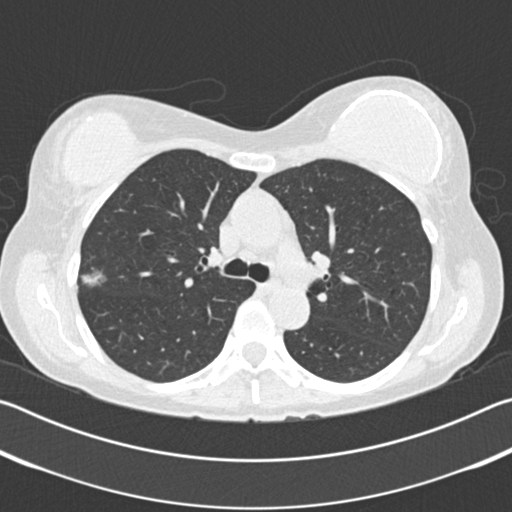
Low-dose screening chest CT, one axial slice; position 123 of 183 along the scan axis; reconstruction kernel B30f; 120 kVp; lung window (W 1500 / L -600 HU); 2 mm slice thickness; 512 × 512 image matrix, field of view 340 × 340 mm.
Outlined on this slice (expert manual segmentation):
- lesion 1 (tumor, upper lobe of right lung): box from (x=81, y=270) to (x=107, y=287) px